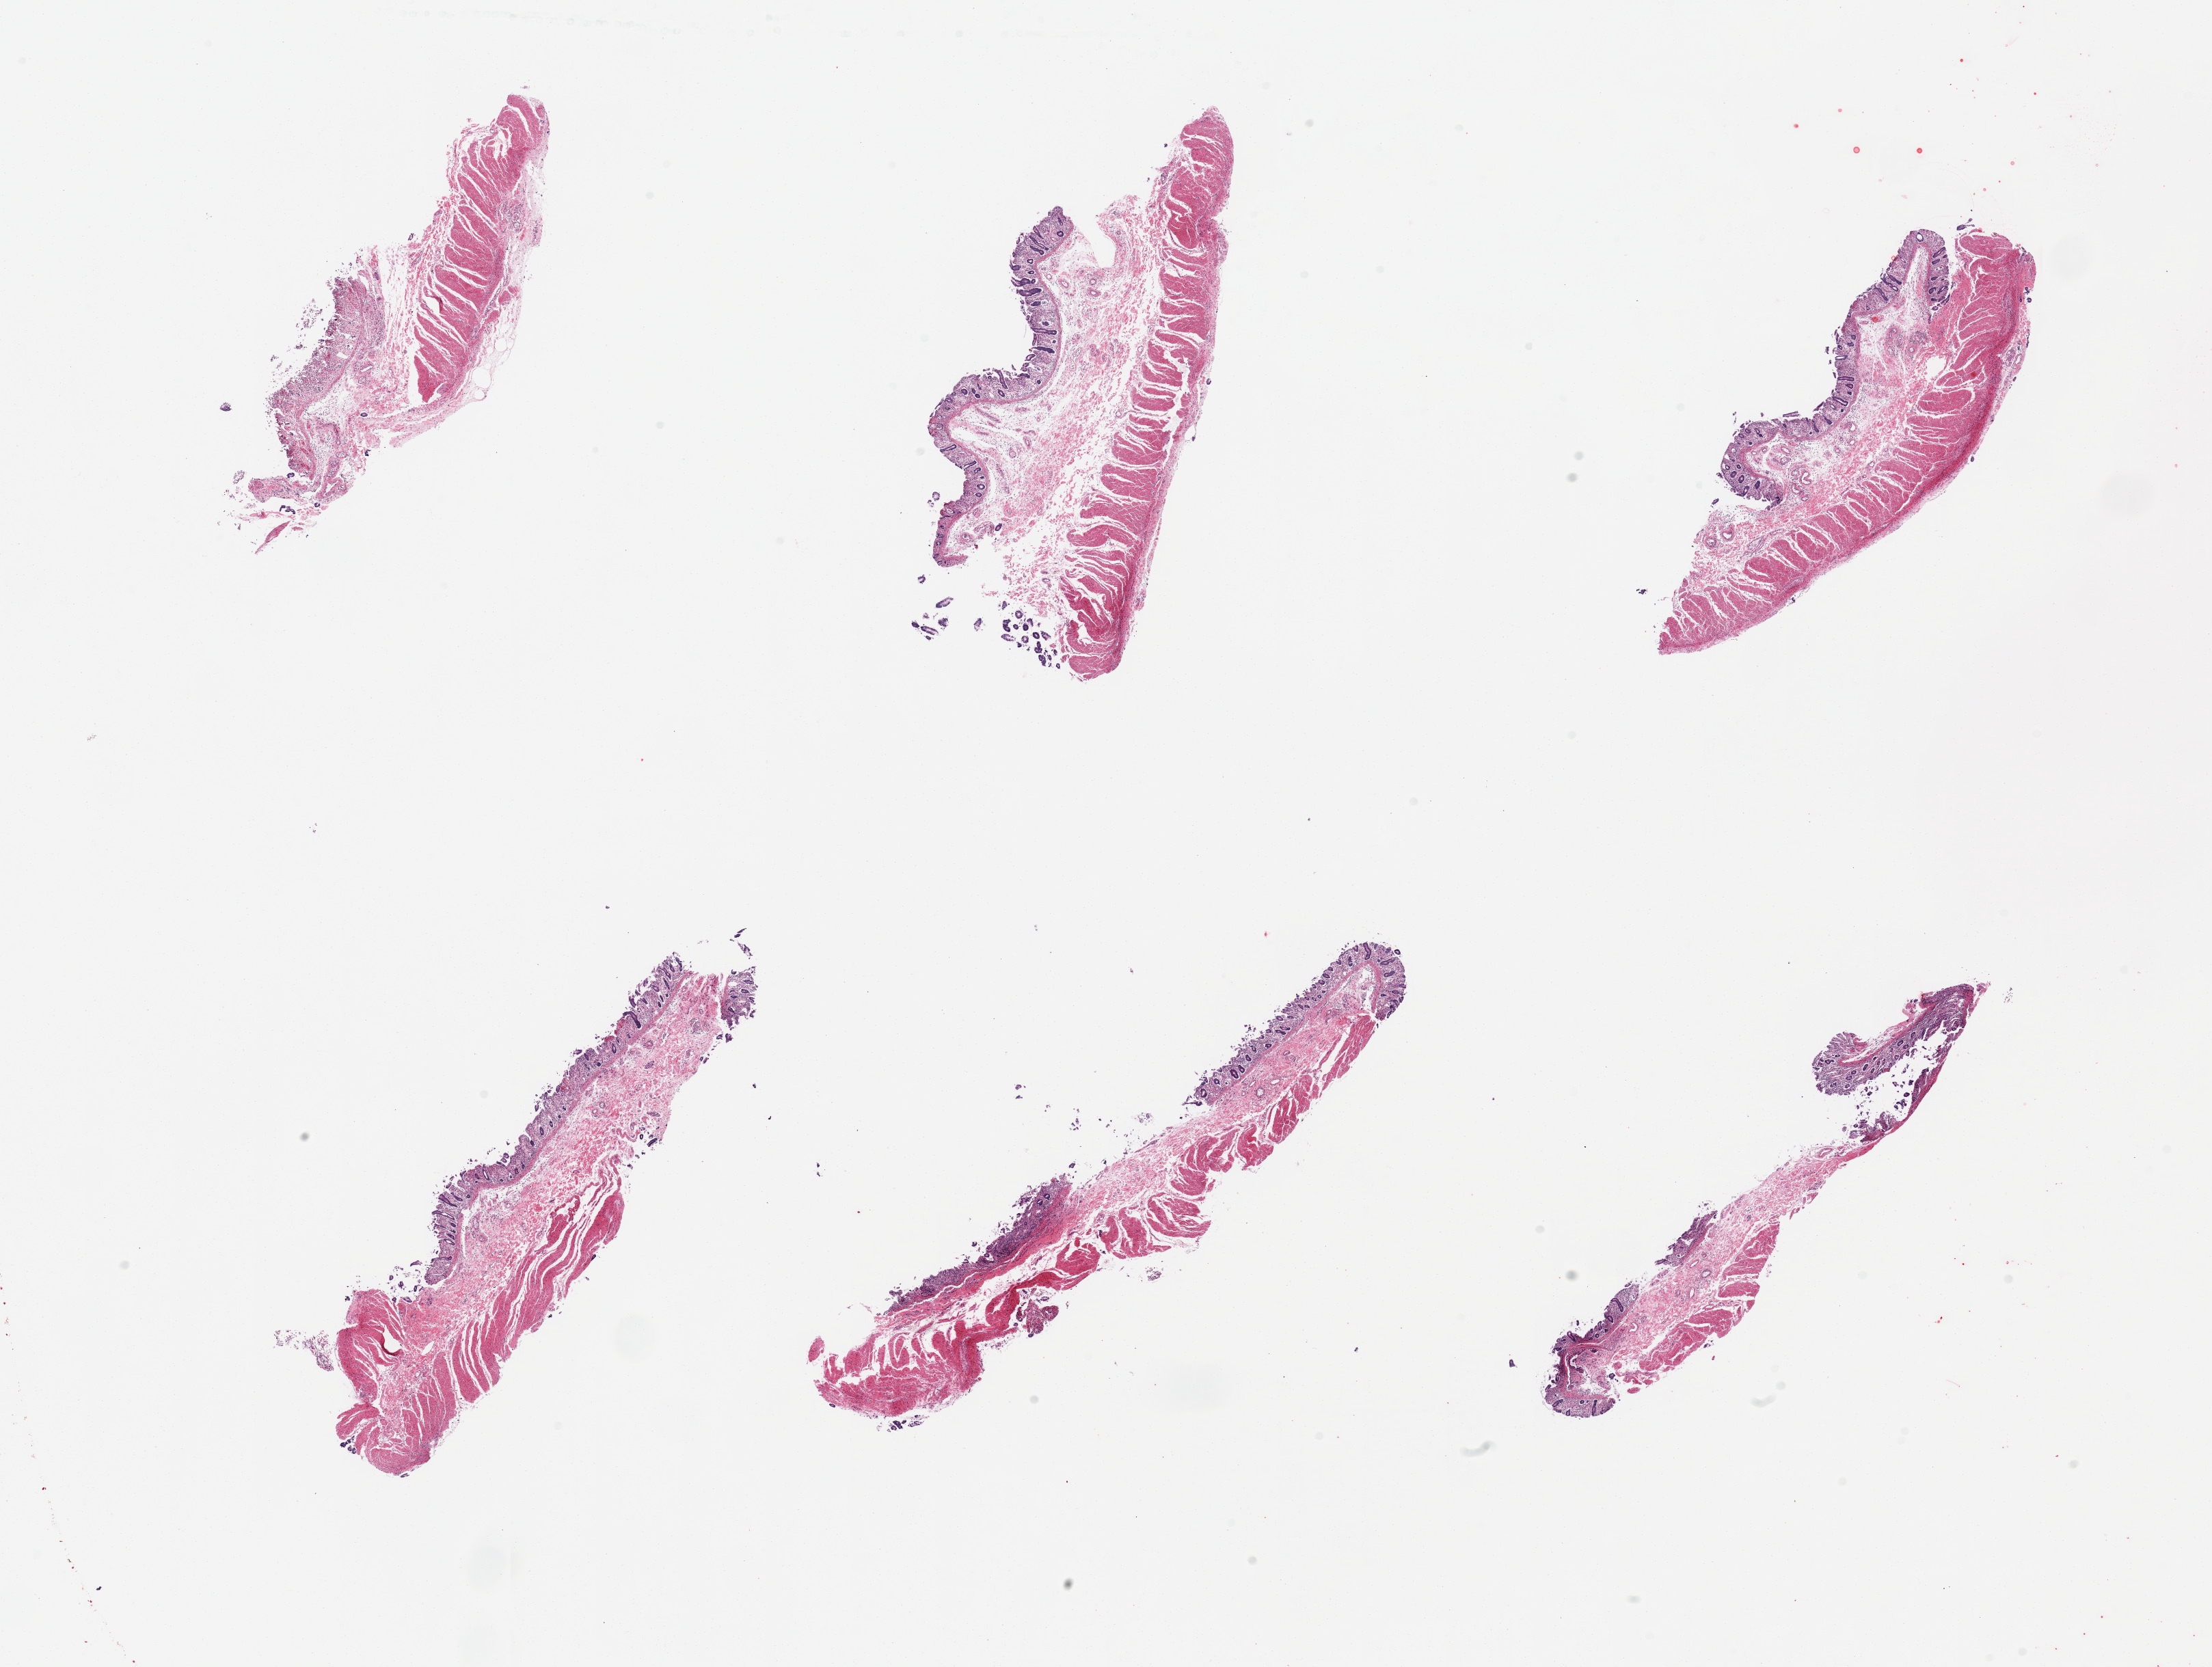
Whole-slide image, haematoxylin and eosin stain, whole scanned area (about 25.6 x 19.3 mm, slide scanned at 20x) shown as a low-resolution overview, PAXgene-fixed, paraffin-embedded tissue, sampled site (target tissue): transverse colon, donor tissue sample. Male donor.
Pathologist's review note for this sample: 6 pieces, mucosa is ~0.3mm, 10-15% thickness, markedly autolyzed.